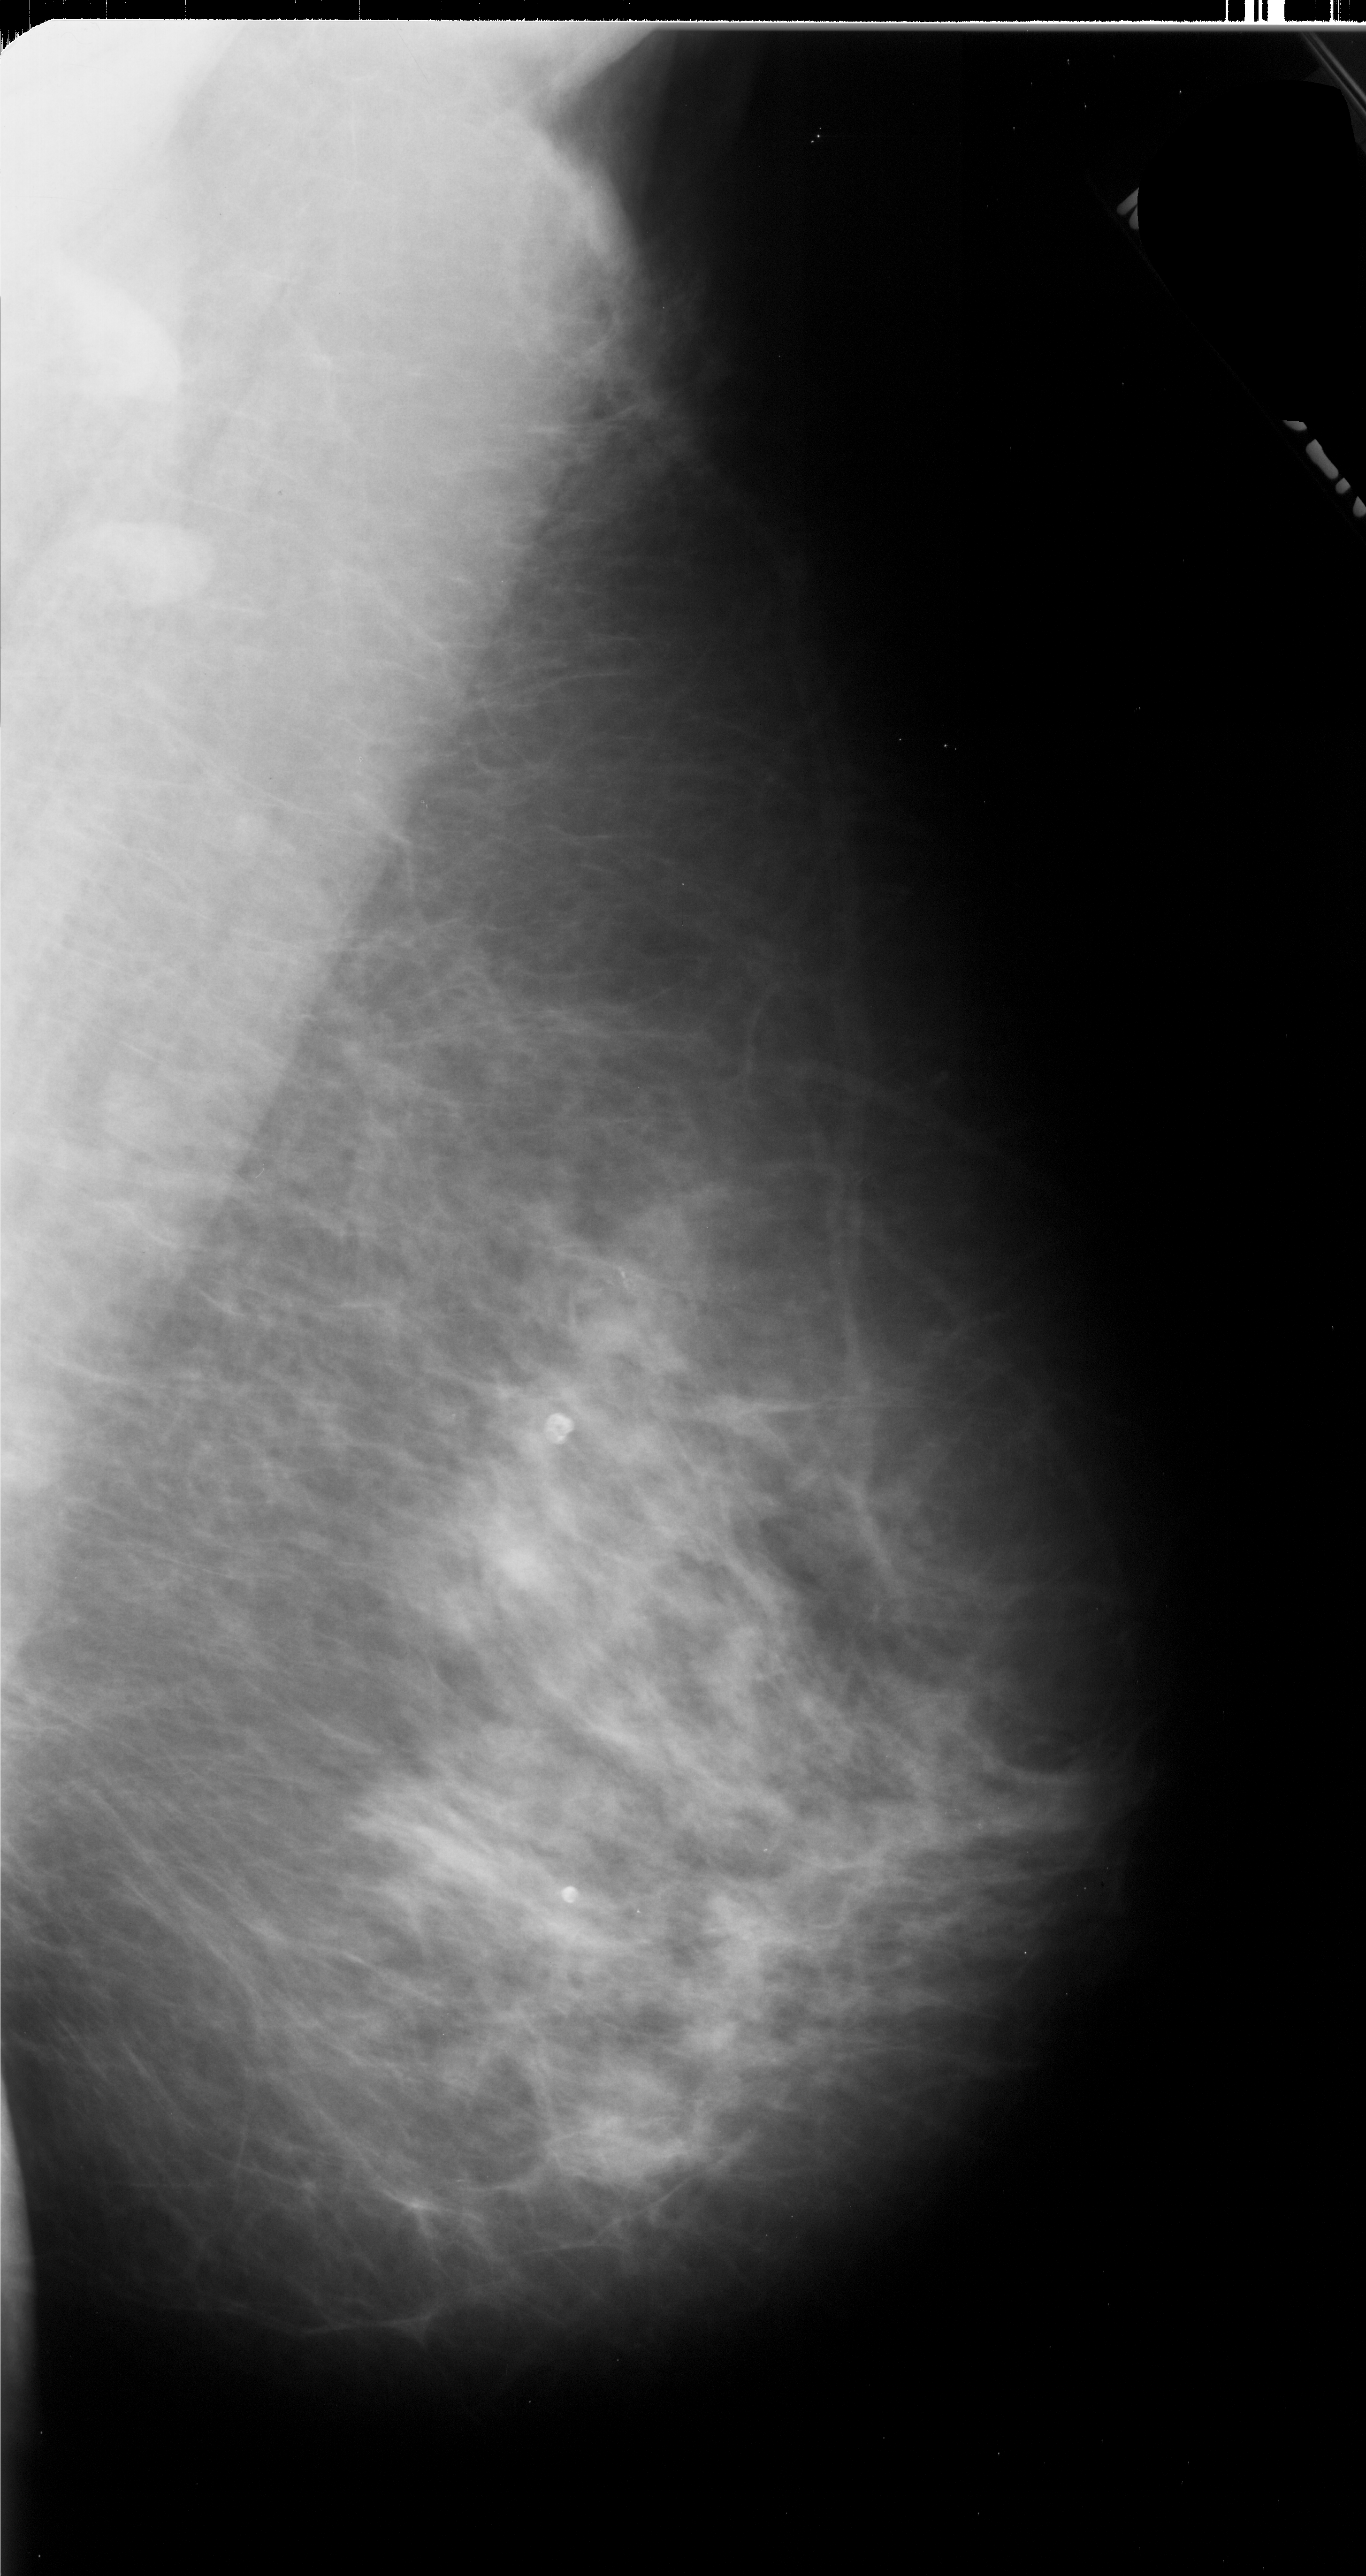
Scanned film-screen mammogram, right breast, mediolateral oblique (MLO) view.
Finding: calcifications, morphology pleomorphic, distribution linear; BI-RADS assessment category 4; pathology (as recorded): malignant.